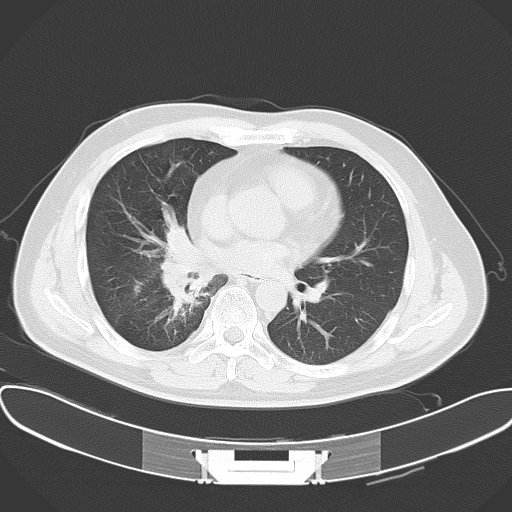
Chest CT, one axial slice. Position 28 of 57 along the scan axis. Reconstruction kernel B70f. 120 kVp. Lung window (W 1500 / L -600 HU). 512 × 512 image matrix. Male patient, age 48 years. From the clinical record (not read from this slice): clinical TNM (as recorded): T1a N1 M1c; histopathological grade: G3.
Structures marked on this image (rectangle marked by the reading radiologist):
- lung tumour (recorded histology: adenocarcinoma): bounding box [x1, y1, x2, y2] px = [155, 219, 206, 319]